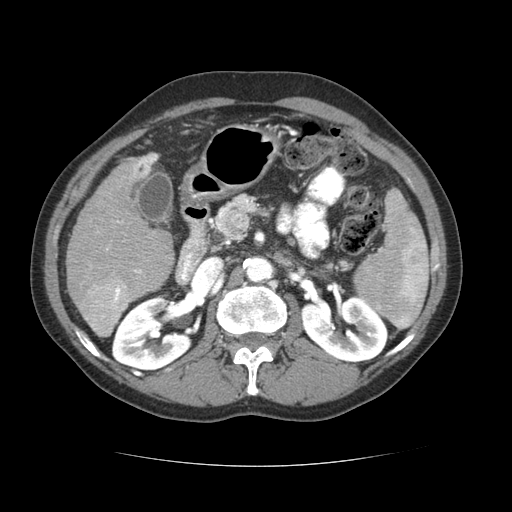
Contrast-enhanced abdominal CT (liver protocol), one axial slice. Position 32 of 69 along the scan axis. Soft-tissue window (W 400 / L 40 HU). 512 × 512 image matrix, field of view 360 × 360 mm. Case-level facts recorded for this patient, not image findings: diagnosis: hepatocellular carcinoma (patient treated with transarterial chemoembolisation; whether this scan precedes or follows treatment is not stated here); TNM stage (as recorded): Stage-II; Child-Pugh class: B; tumour differentiation: poorly differentiated; tumour nodularity: multinodular.
Structures marked on this image (semi-automatically segmented with operator editing):
- liver parenchyma outside the tumour (the mass and vessels are separate outlines, so this box may not span the whole liver): bounding box (x1, y1, x2, y2) in pixels: (66, 152, 174, 336)
- mass: (80, 273, 140, 334)
- liver vessels: (118, 154, 158, 274)